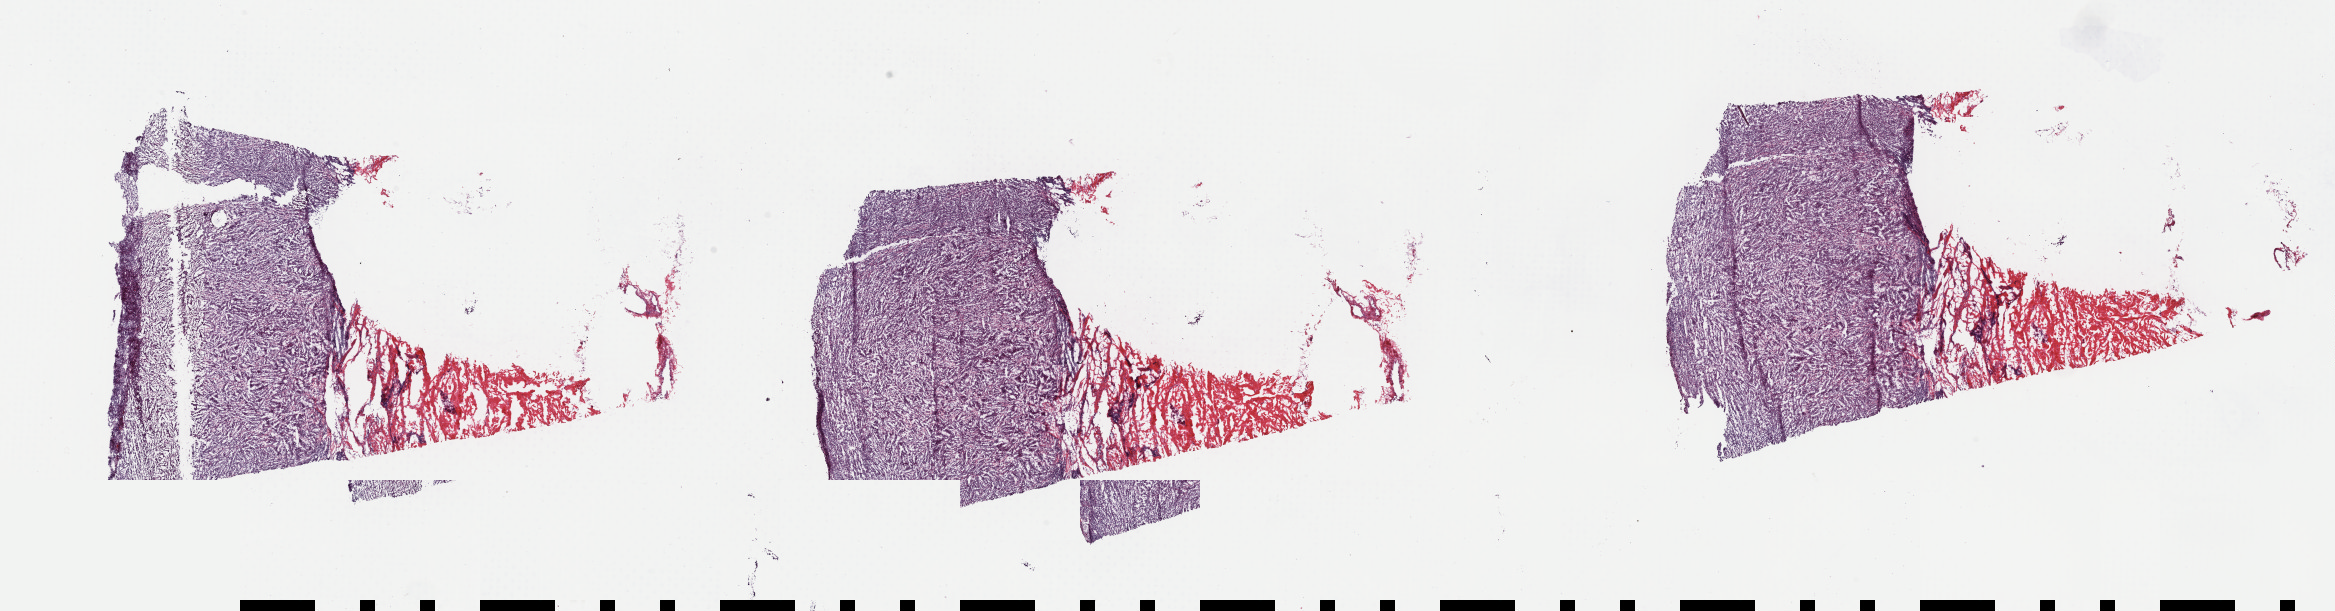
Digitized H&E-stained tissue section (whole slide), shown as a low-resolution overview of the whole scanned area (about 36.8 x 9.6 mm, from a 40x scan). Frozen section. Skin, primary tumour sample. Male, age 77 years at initial diagnosis. Slide review estimates, as recorded: tumour cells 80%, tumour nuclei 80%, normal cells 20%, stromal cells 0%, necrosis 0%. Inflammatory infiltration, as recorded: lymphocyte infiltration 3%, monocyte infiltration 0%, neutrophil infiltration 0%.
Histologic diagnosis: Malignant melanoma, NOS. AJCC pathologic stage: IIB (7th edition).